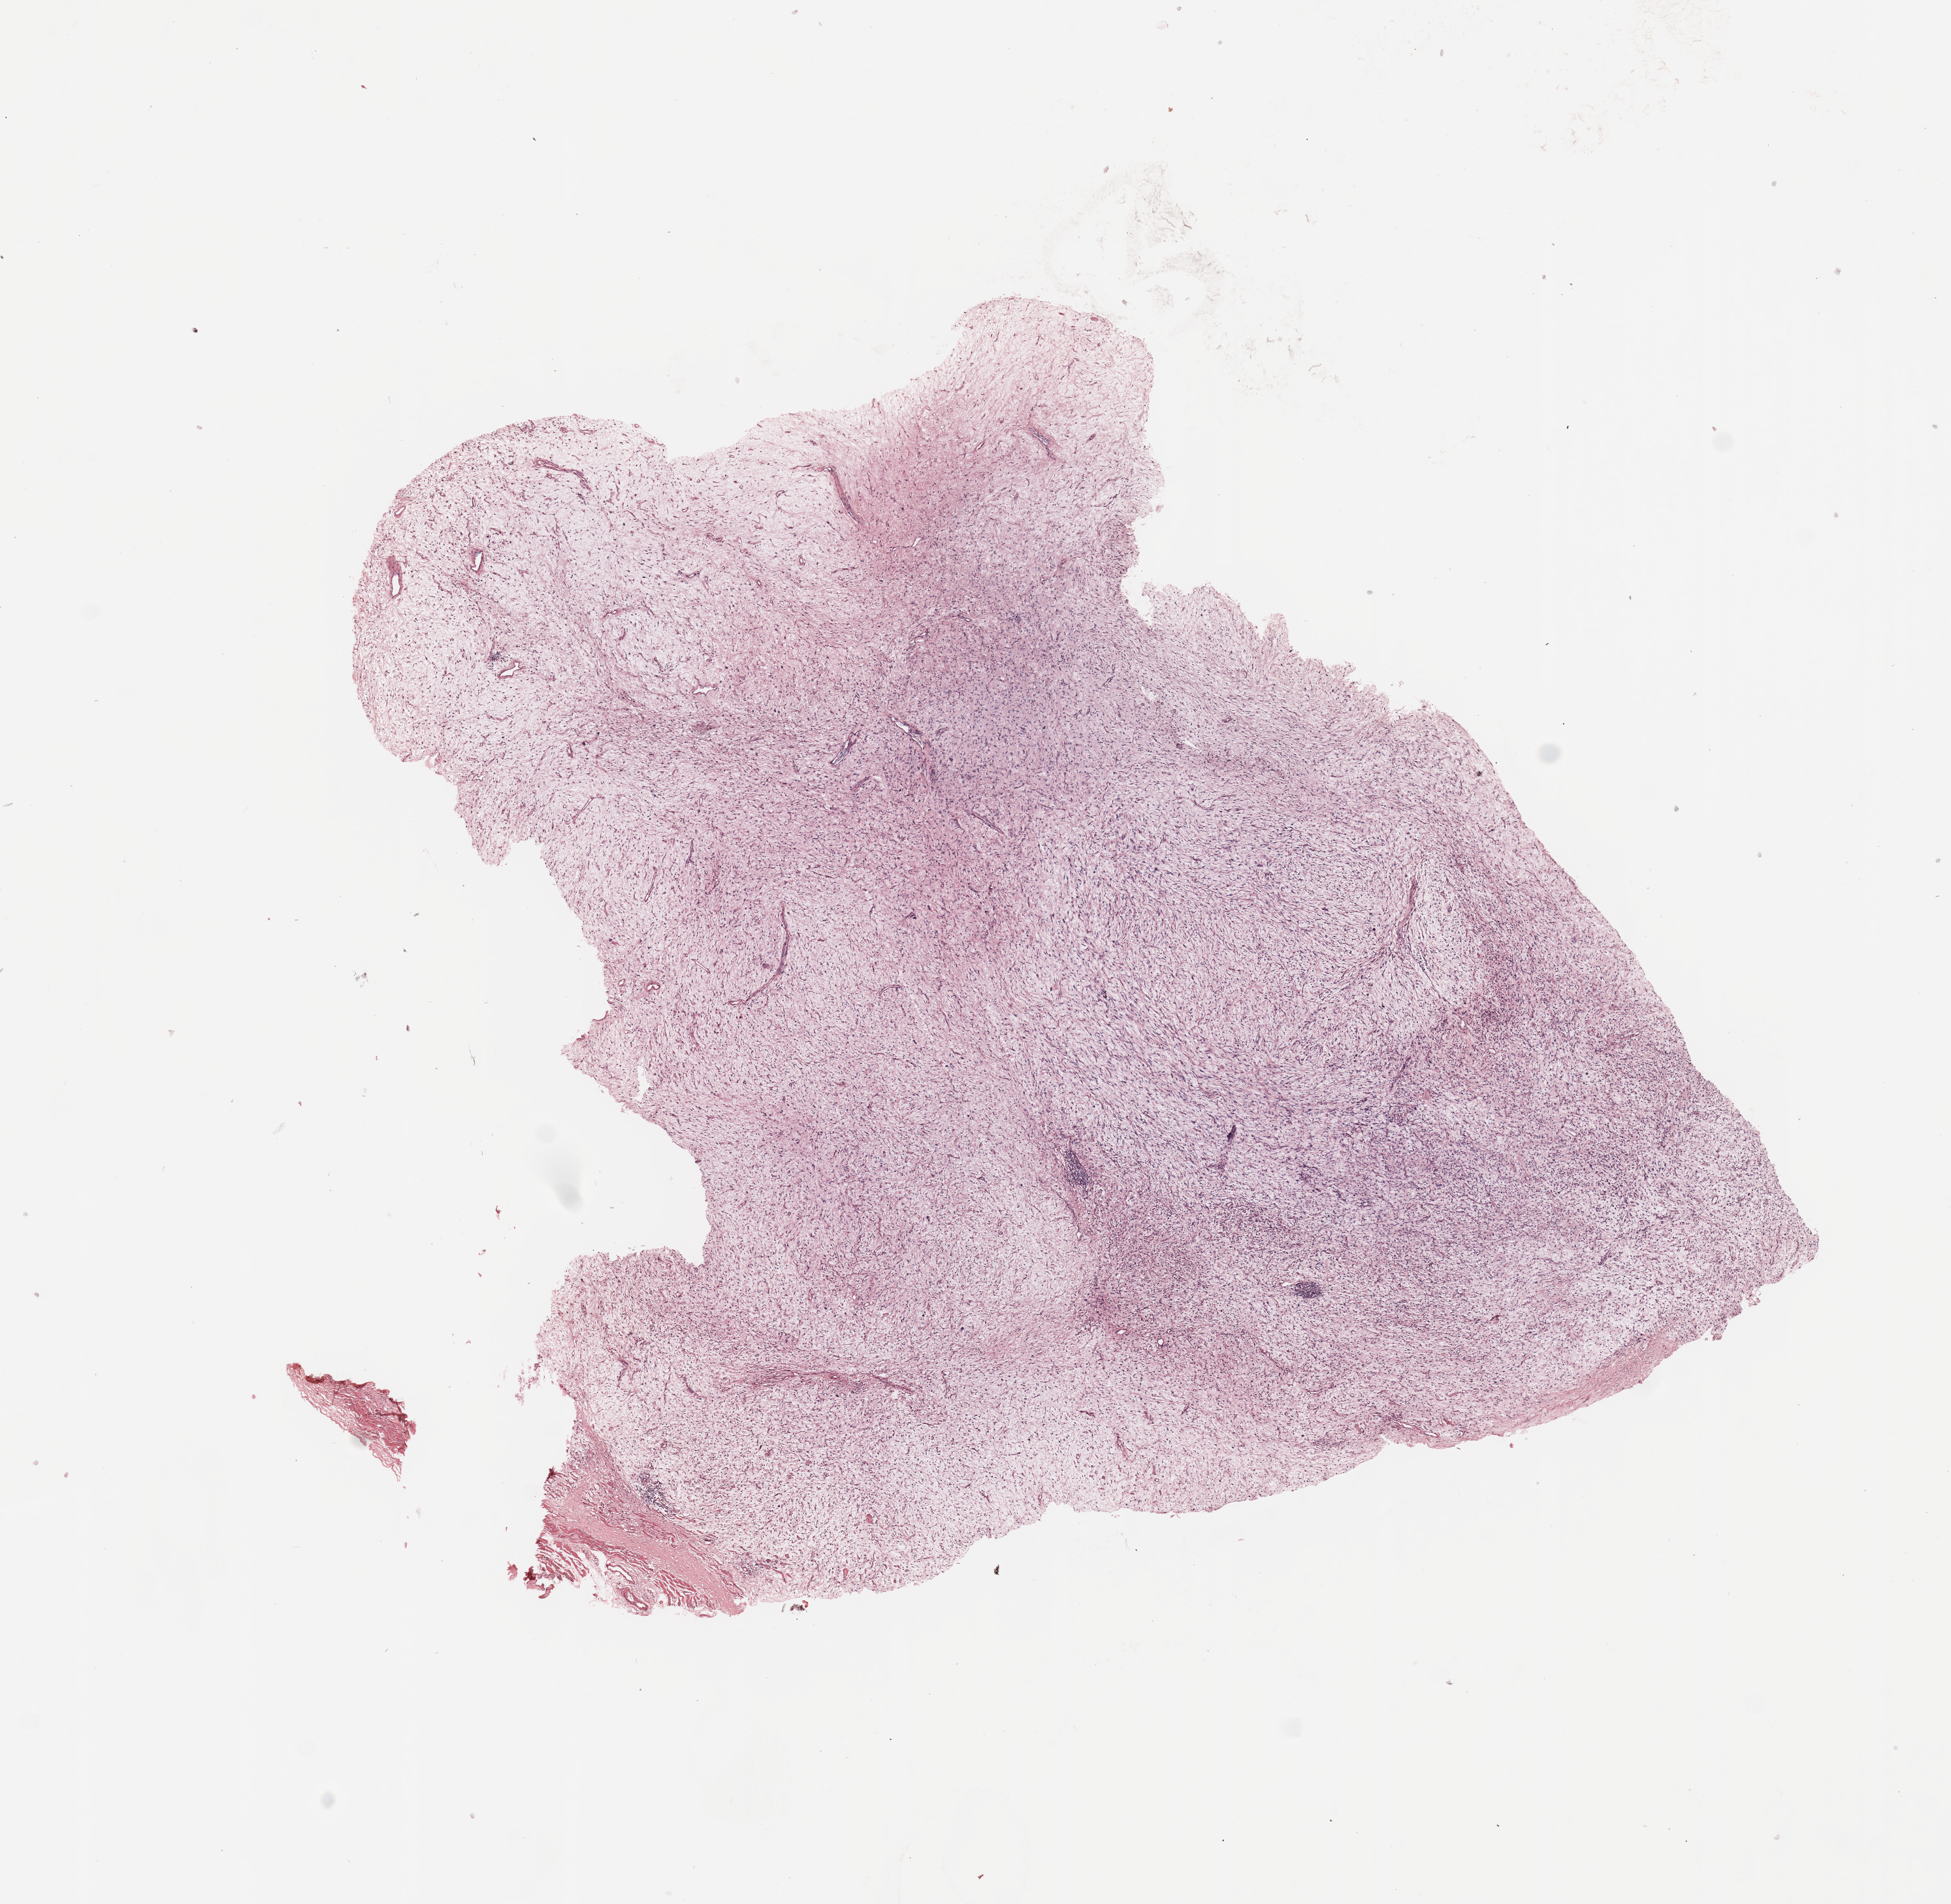
H&E whole-slide image — a low-resolution overview of the entire scanned area, about 11.8 x 11.5 mm, tumour tissue sample. Female, 77 y/o.
Primary tumour site (as recorded): lower extremity. Patient diagnosis (cohort enrolment): sarcoma (site not recorded at cohort level).